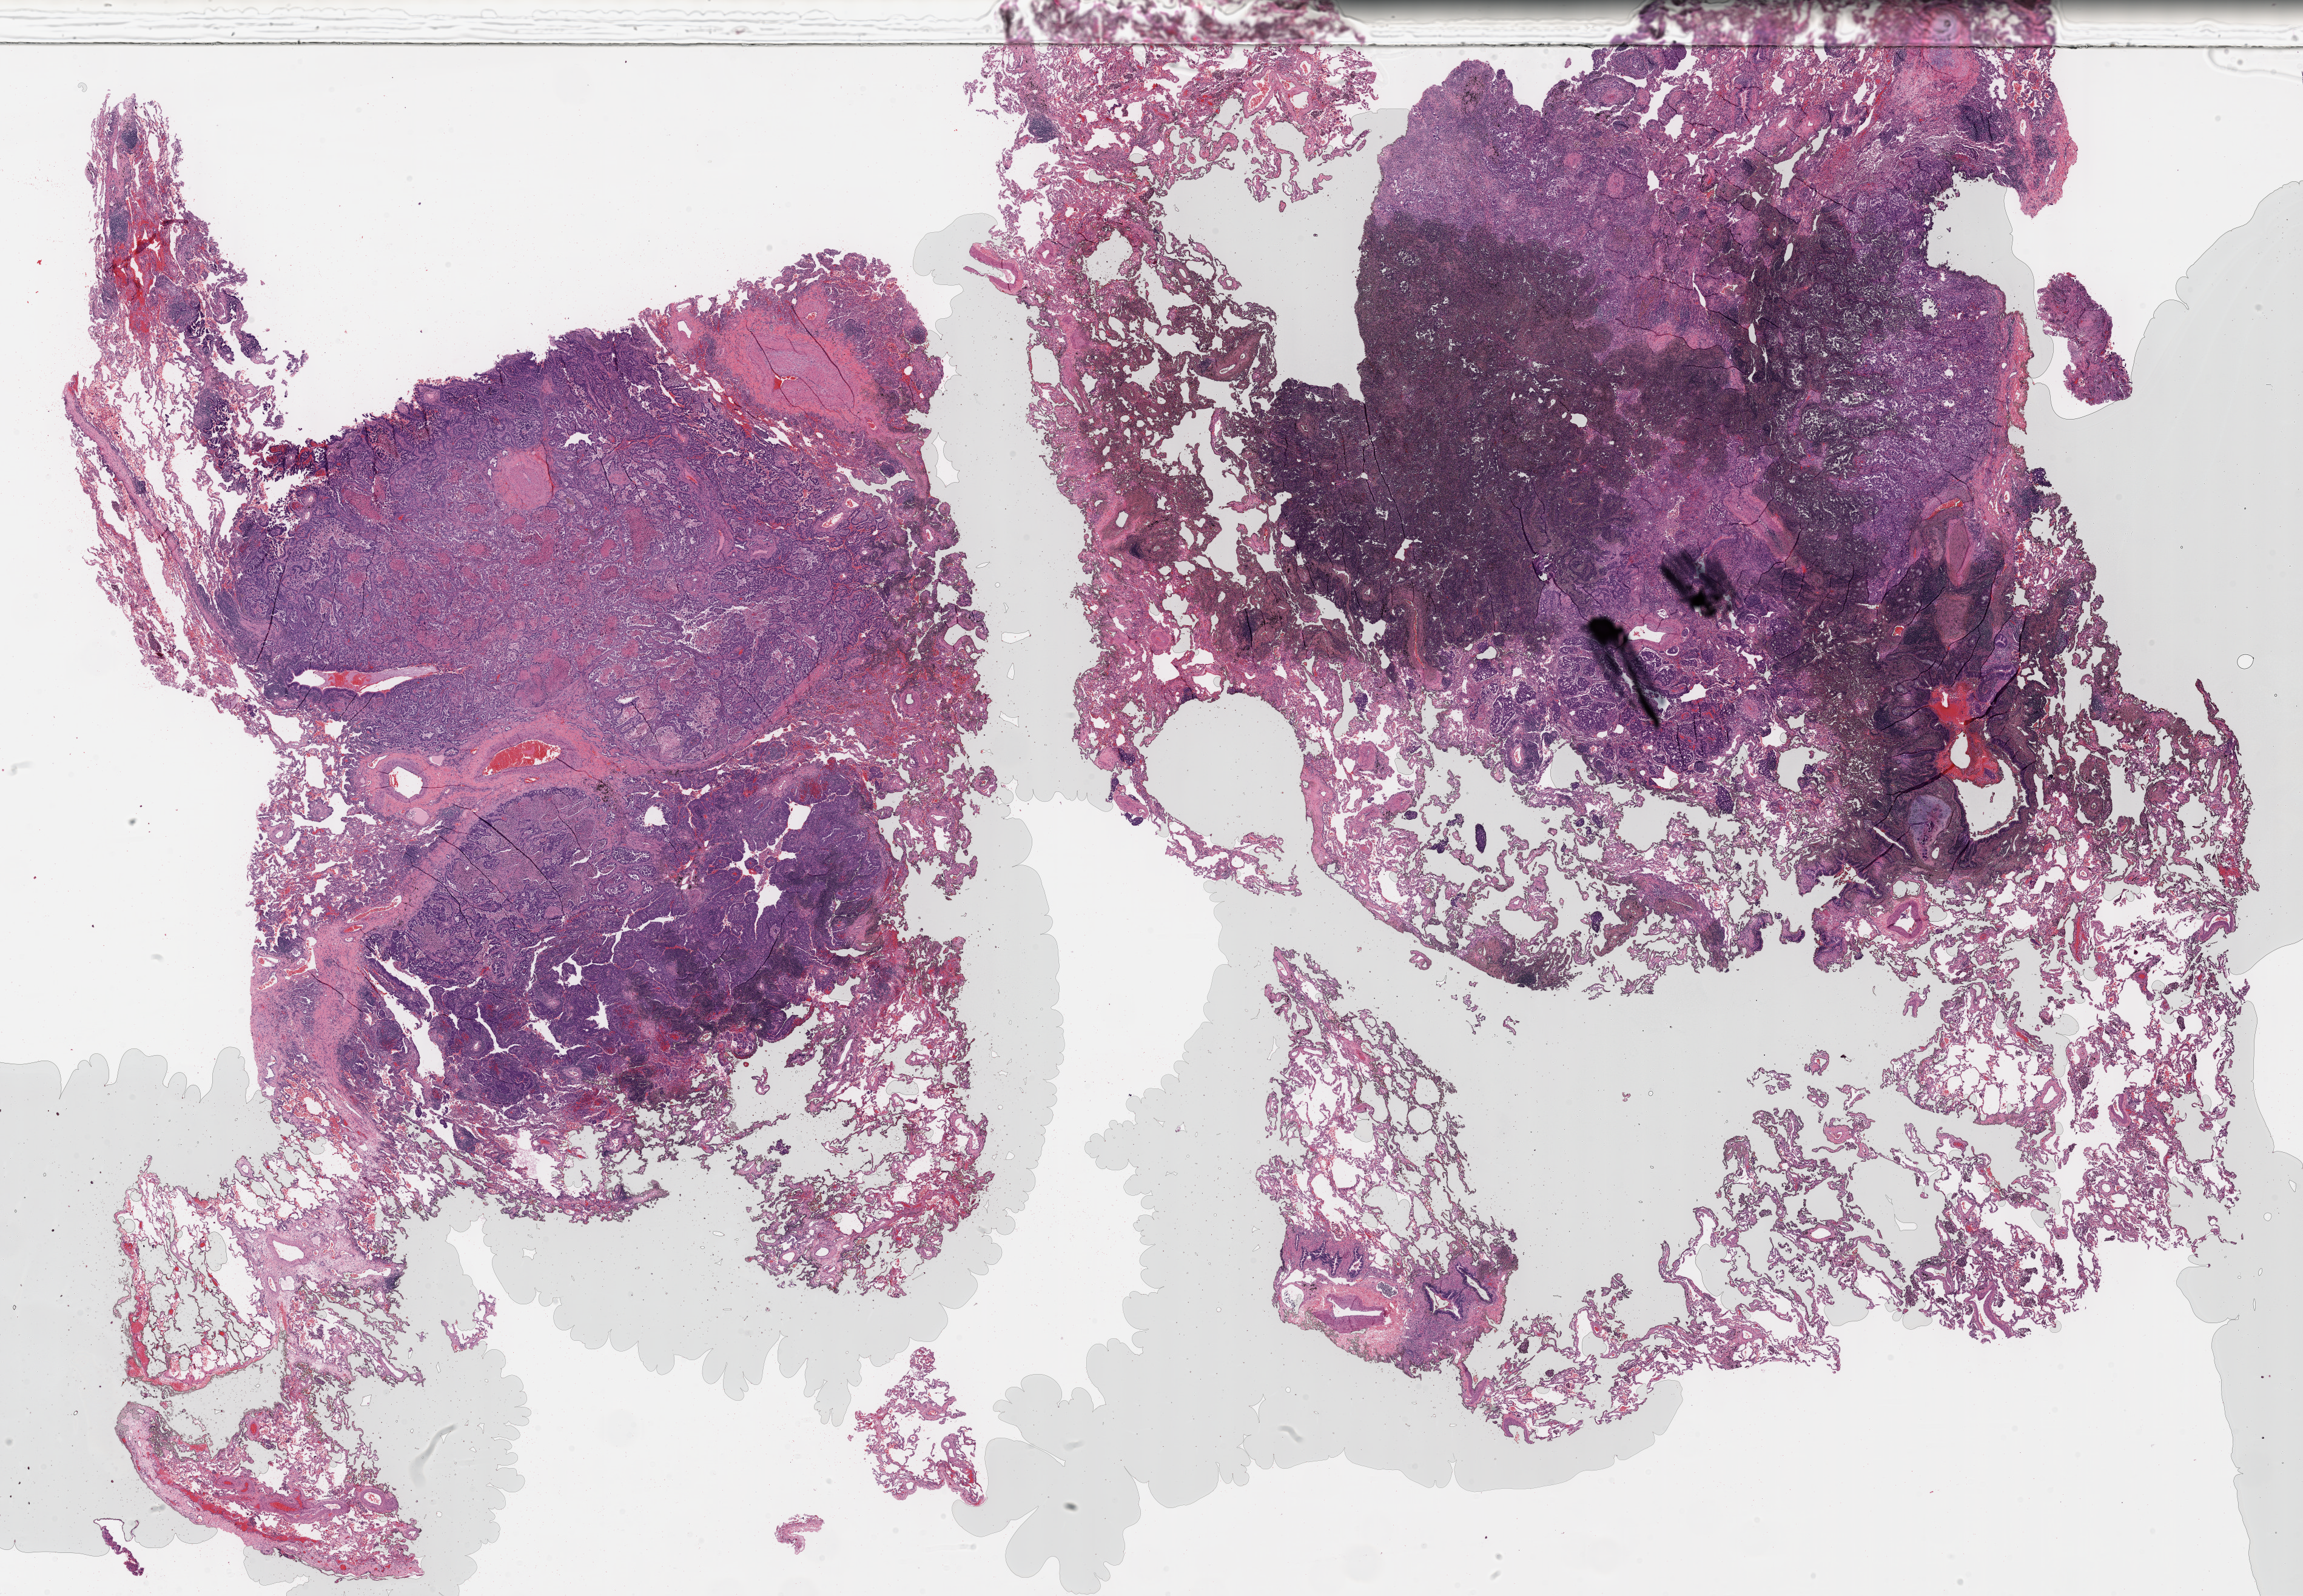
Whole-slide histology image, H&E-stained — shown as a low-resolution overview of the whole scanned area (about 30.7 x 21.3 mm, from a 40x scan); FFPE section; primary tumour sample from the lung. Male patient; age at initial diagnosis 62 years.
* histologic diagnosis: Adenocarcinoma with mixed subtypes (upper lobe, lung)
* AJCC pathologic stage: IA
* laterality: right